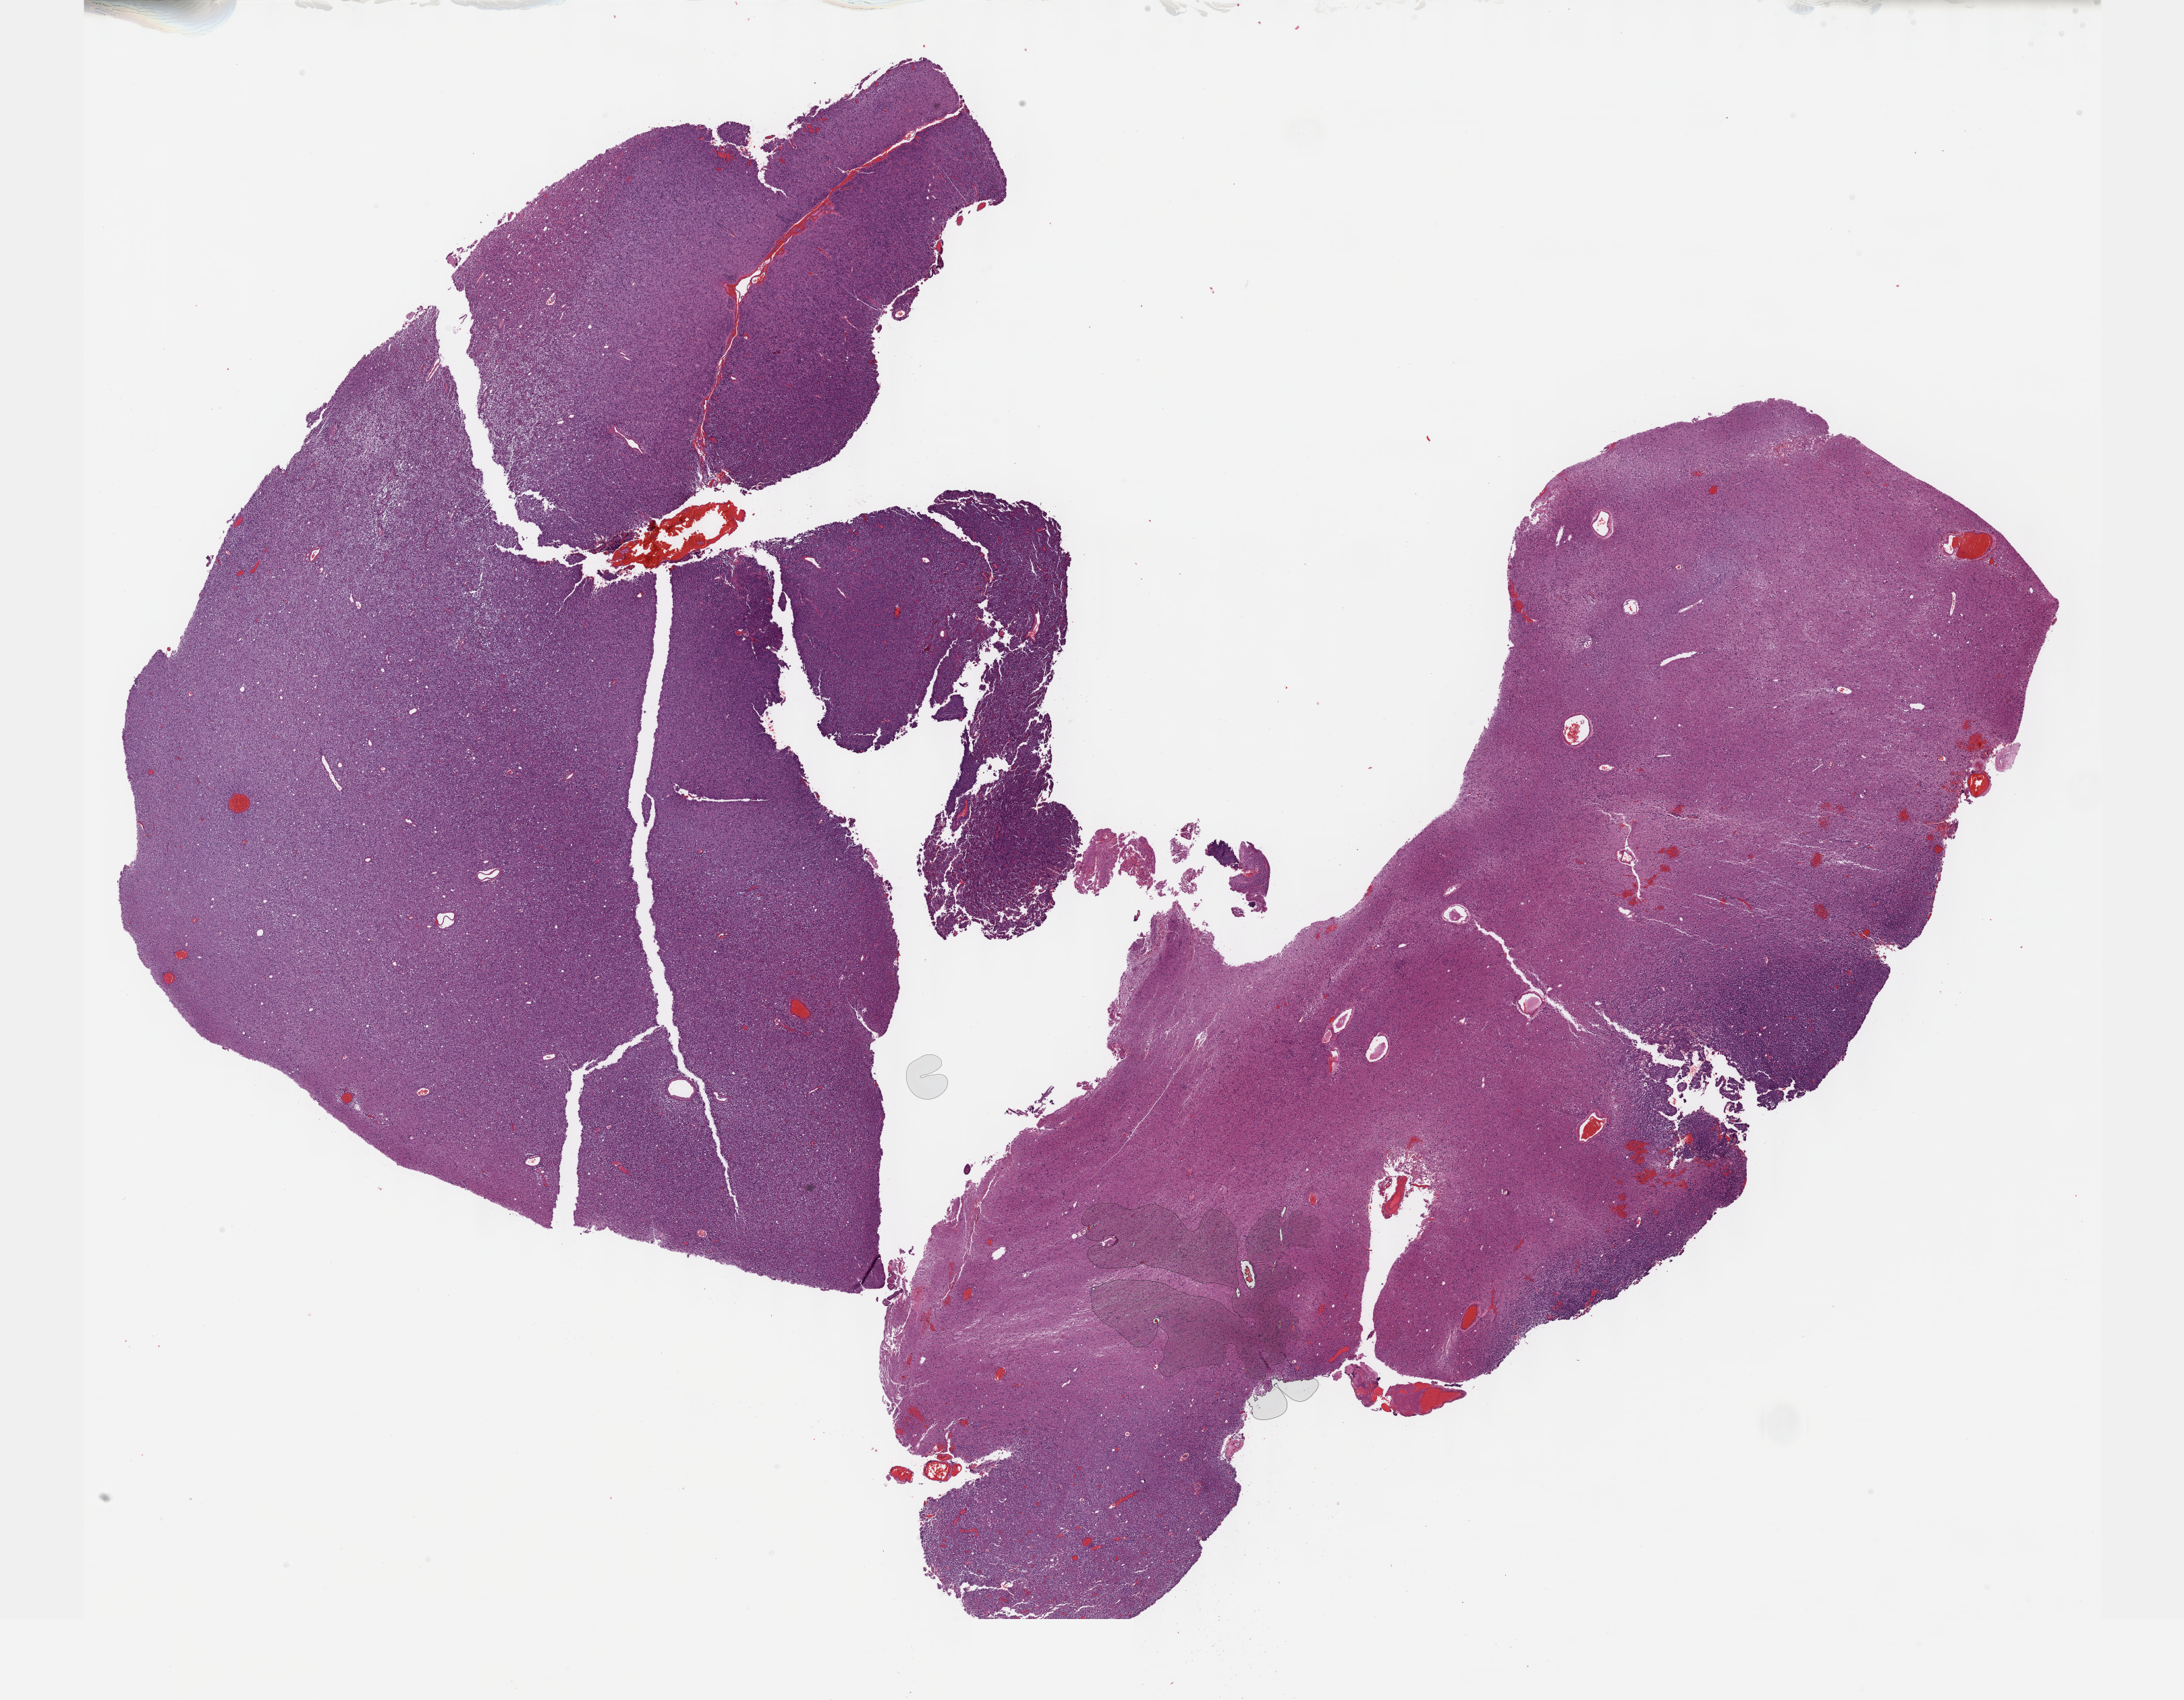
Digitized H&E tissue section (whole slide) — low-resolution overview of the scanned area, about 26.2 x 20.4 mm (acquisition: 40x scan), formalin-fixed paraffin-embedded (FFPE) diagnostic section, brain, primary tumour sample. Male patient; age at initial diagnosis 59 years. Histologic grade: G3 (poorly differentiated).
• histologic diagnosis: Oligodendroglioma, anaplastic (cerebrum)
• laterality: left